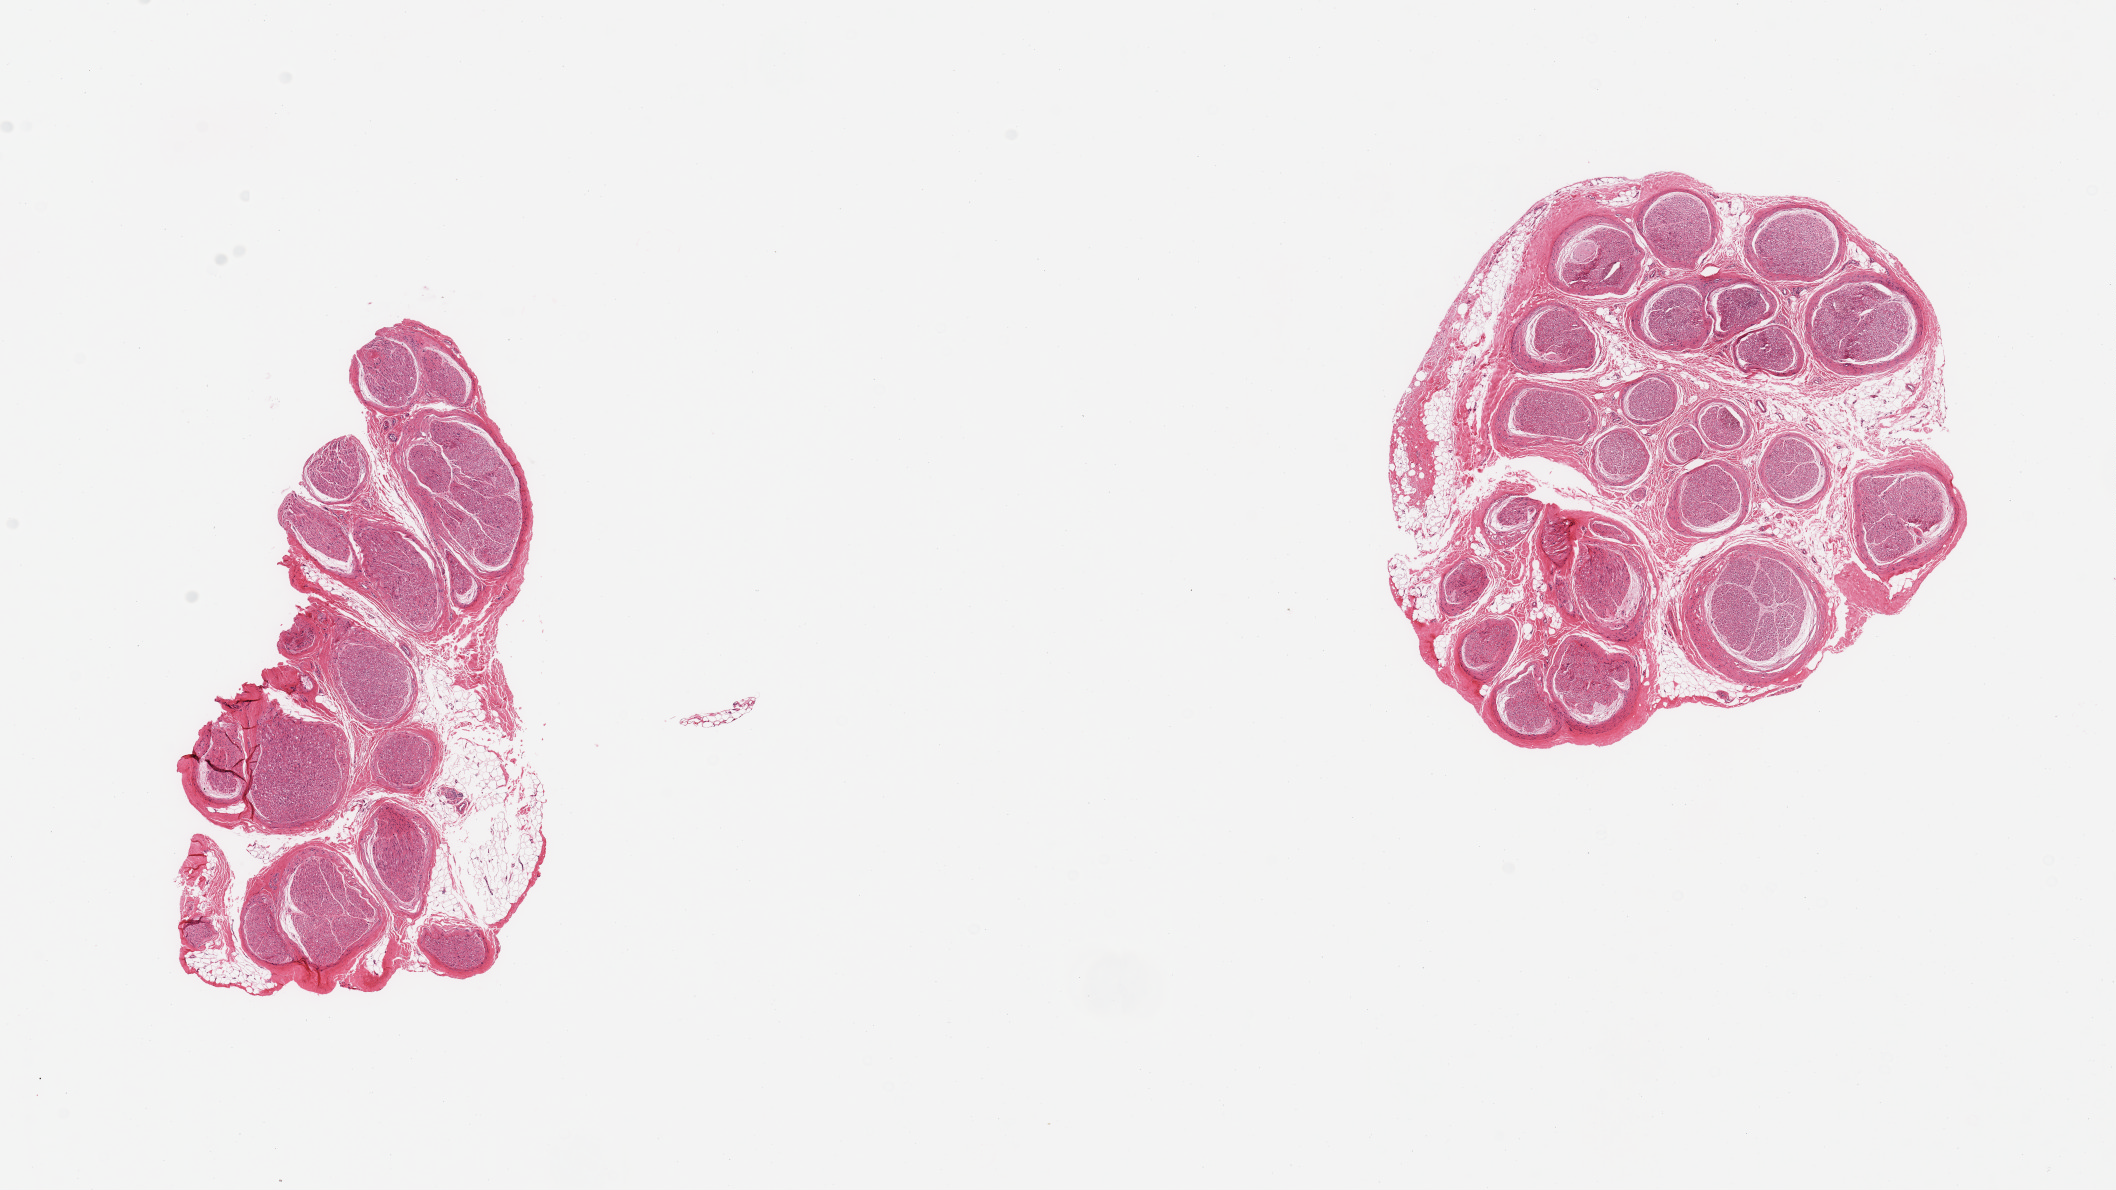
Whole-slide image, hematoxylin and eosin (H&E) stain, shown as a low-resolution overview of the whole scanned area (about 16.7 x 9.4 mm); PAXgene-fixed paraffin-embedded (PFPE) section; target tissue: tibial nerve; tissue donor sample.
Review note (as recorded): 2 pieces, single nubbin adherent fat up to ~0.8mm.